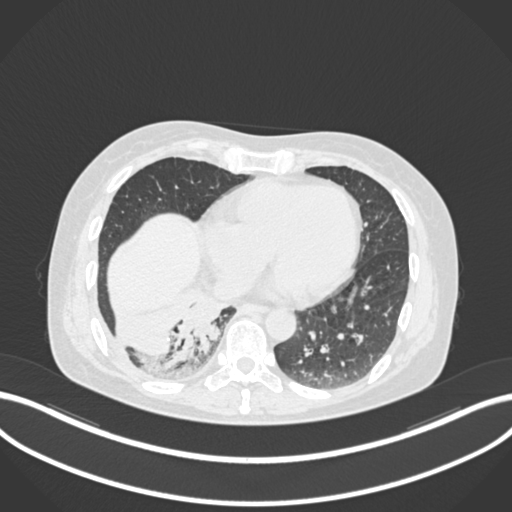
Chest CT, one axial slice. Slice 45 of 168 in the series (ordered by position). Lung window (W 1500 / L -600 HU). 1 mm slice thickness. 512 × 512 image matrix, field of view 400 × 400 mm. Patient: female, 63 years. From the clinical record (not read from this slice): clinical TNM (as recorded): T1c N0 M0.
Annotated regions visible in this slice (bounding box drawn by a radiologist):
- lung tumour (recorded histology: adenocarcinoma): bounding box <164,297,222,370> (left, top, right, bottom; pixels)